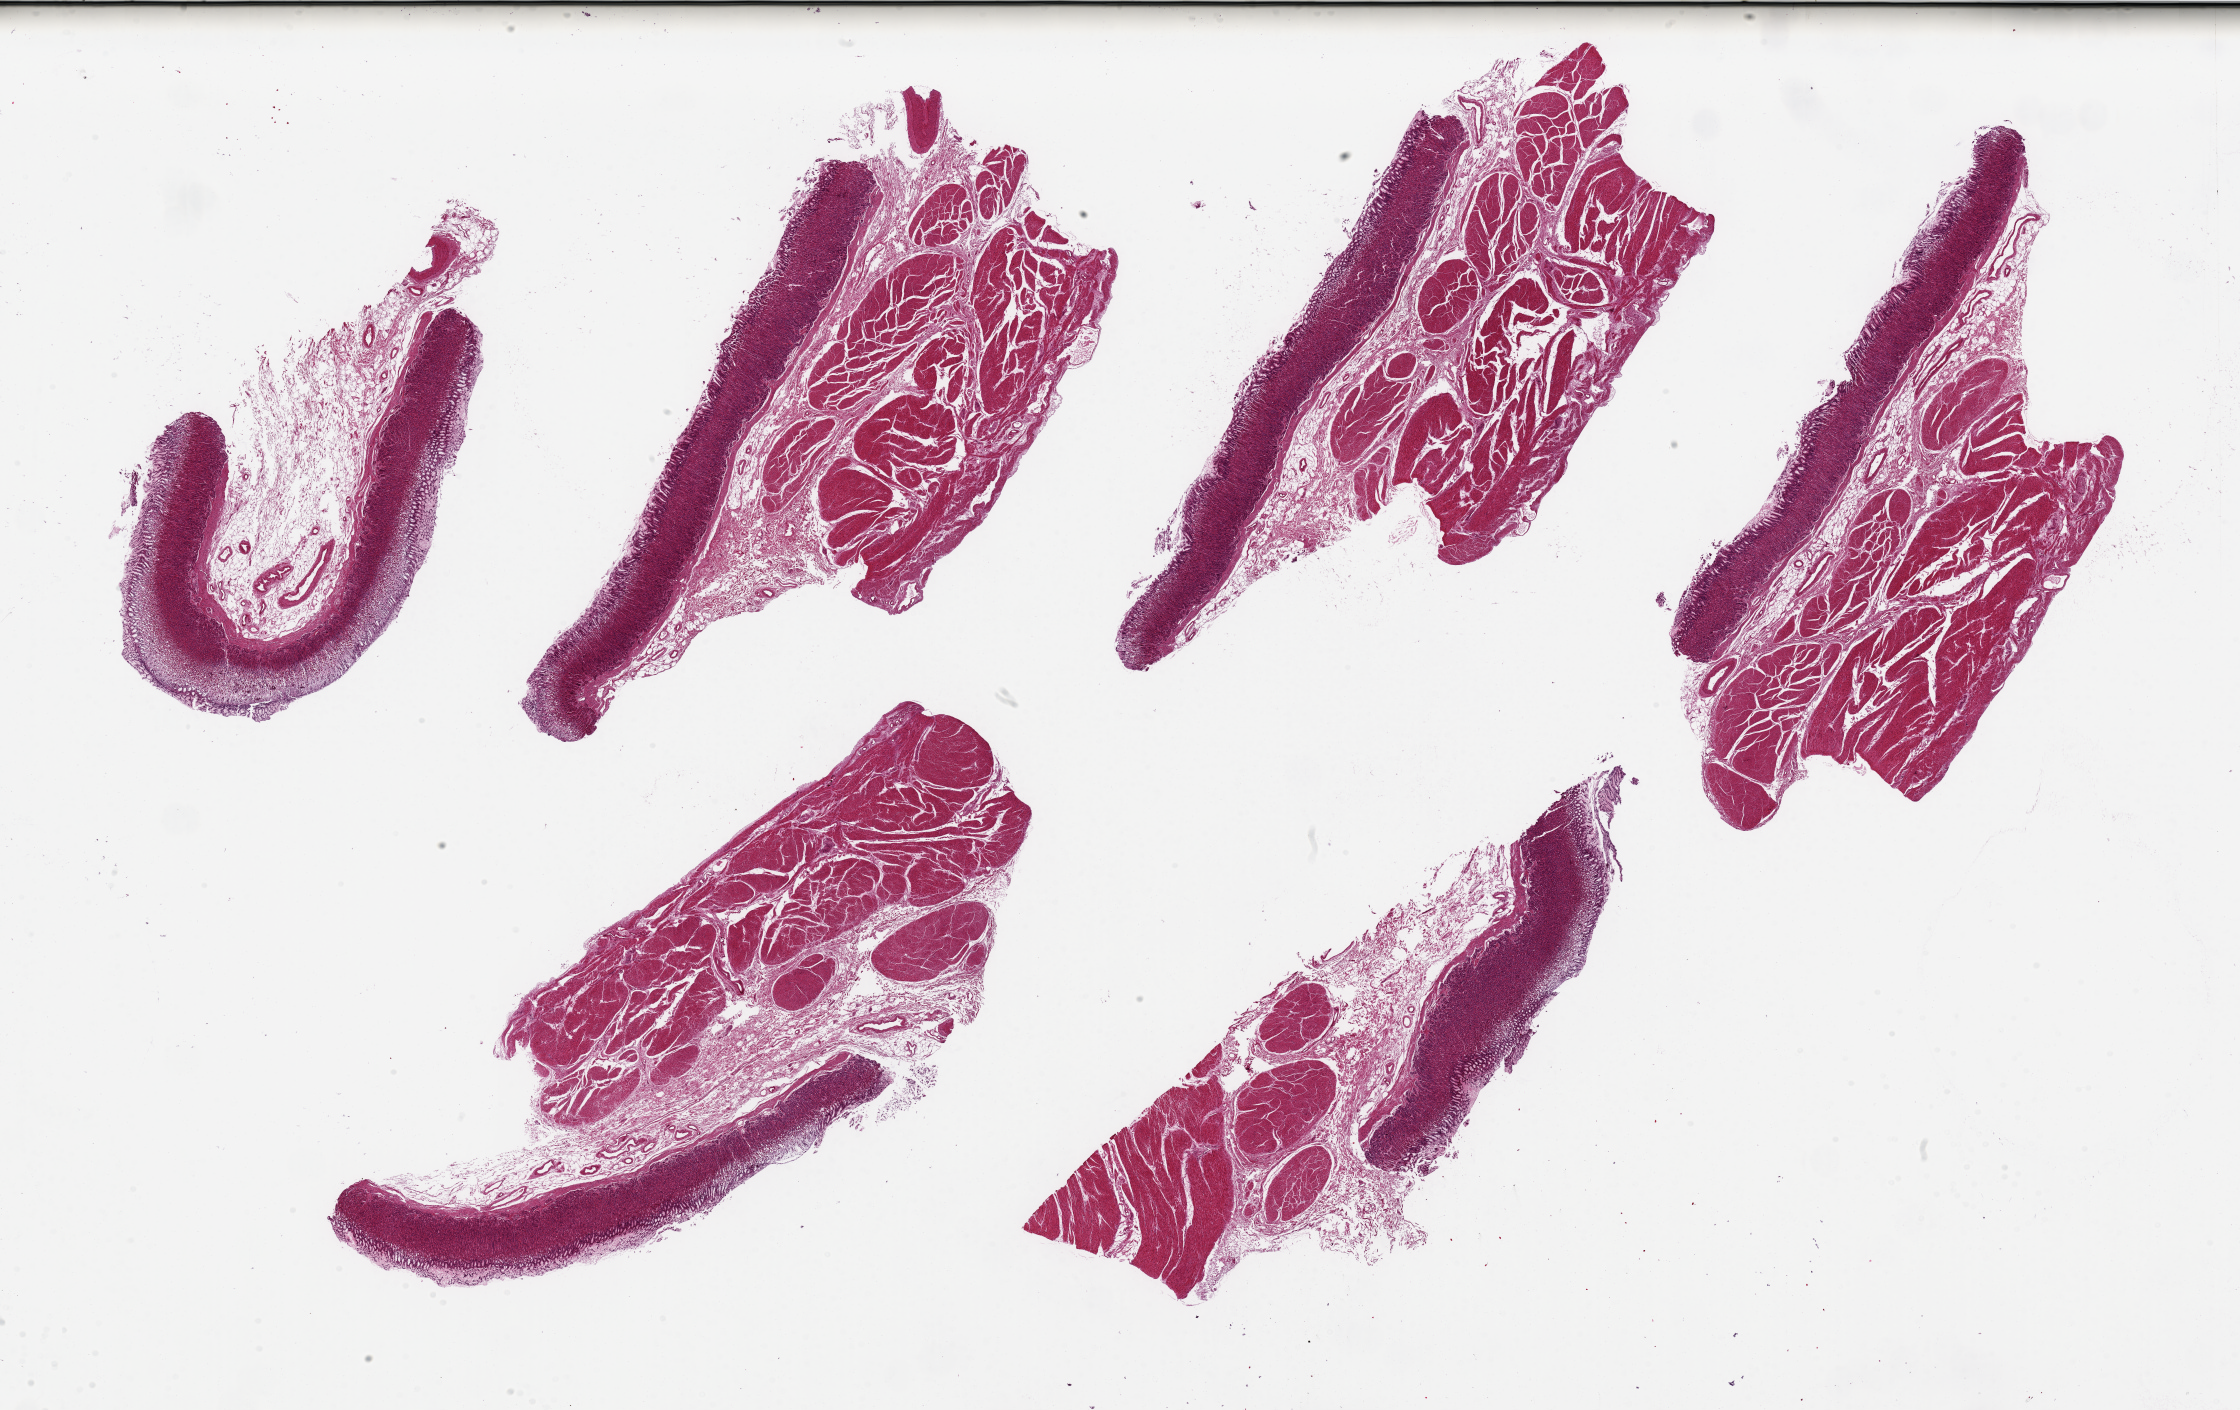
Digitized hematoxylin and eosin (H&E)-stained section, brightfield, a low-resolution overview of the entire scanned area, about 35.4 x 22.3 mm (slide scanned at 20x). PAXgene-fixed, paraffin-embedded tissue. Target tissue: stomach. Tissue donor sample. Male donor.
Review note (as recorded): 6 pieces up to 11x5 mm; deep oxyntic mucosa better preserved than surface; varies from piece to piece.